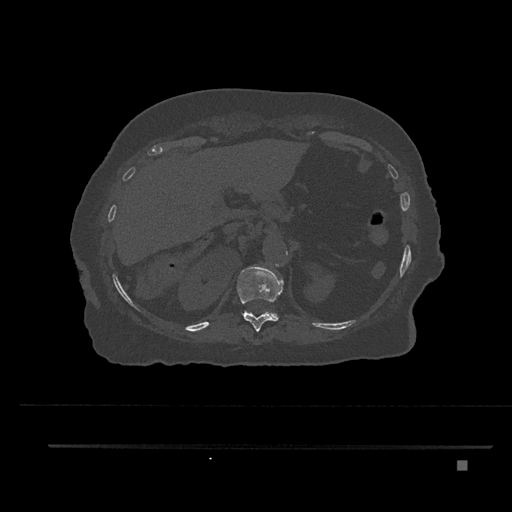
CT including the spine, one axial slice. Position 304 of 797 along the scan axis. Bone window (W 1800 / L 400 HU). 0.5 mm slice thickness. 512 × 512 image matrix, field of view 437 × 437 mm. Female patient, age 76 years. From the clinical record (not read from this slice): primary cancer: lung; vertebrae with lytic lesions (as recorded): T11, L3.
Structures marked on this image (semi-automatic segmentation, software-assisted and operator-edited):
- T11 vertebra: bounding box [x1, y1, x2, y2] px = [237, 265, 283, 332]
- T12 vertebra: [263, 311, 279, 319]